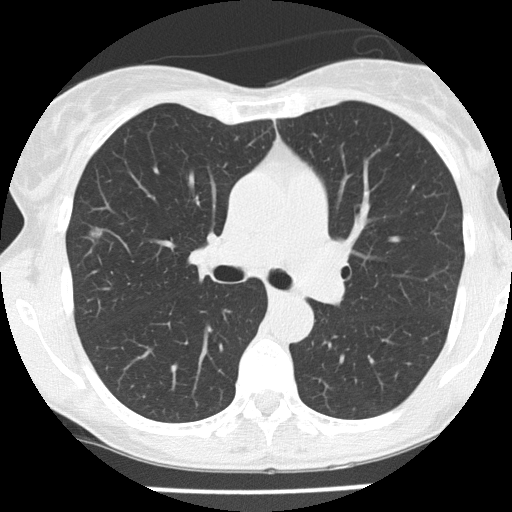
Axial slice from a low-dose chest CT screening exam. Baseline annual screen. Lung window (W 1500 / L -600 HU). Lung (sharp) reconstruction kernel (FC51). 120 kVp. Slice 62 of 166 in the series. Female participant, aged 56 years at enrolment. Former smoker at enrolment.
Lesion marked by an expert reader, bounding box (x1, y1, x2, y2) in pixels: (79, 220, 115, 248). Screening reader's record for this exam (one nodule recorded; not confirmed to be the boxed lesion): non-calcified nodule or mass ≥4 mm, right upper lobe, 7 × 5 mm, poorly defined margins, ground glass attenuation. Official screen result: positive, change unspecified: nodule(s) >= 4 mm or enlarging nodule(s), mass(es), or other non-specific abnormalities suspicious for lung cancer. Later outcome: lung cancer diagnosed 148 days after this screen — bronchiolo-alveolar carcinoma, non-mucinous, right upper lobe, well differentiated (G1), stage IA (AJCC 6th edition), 6 mm at pathology.